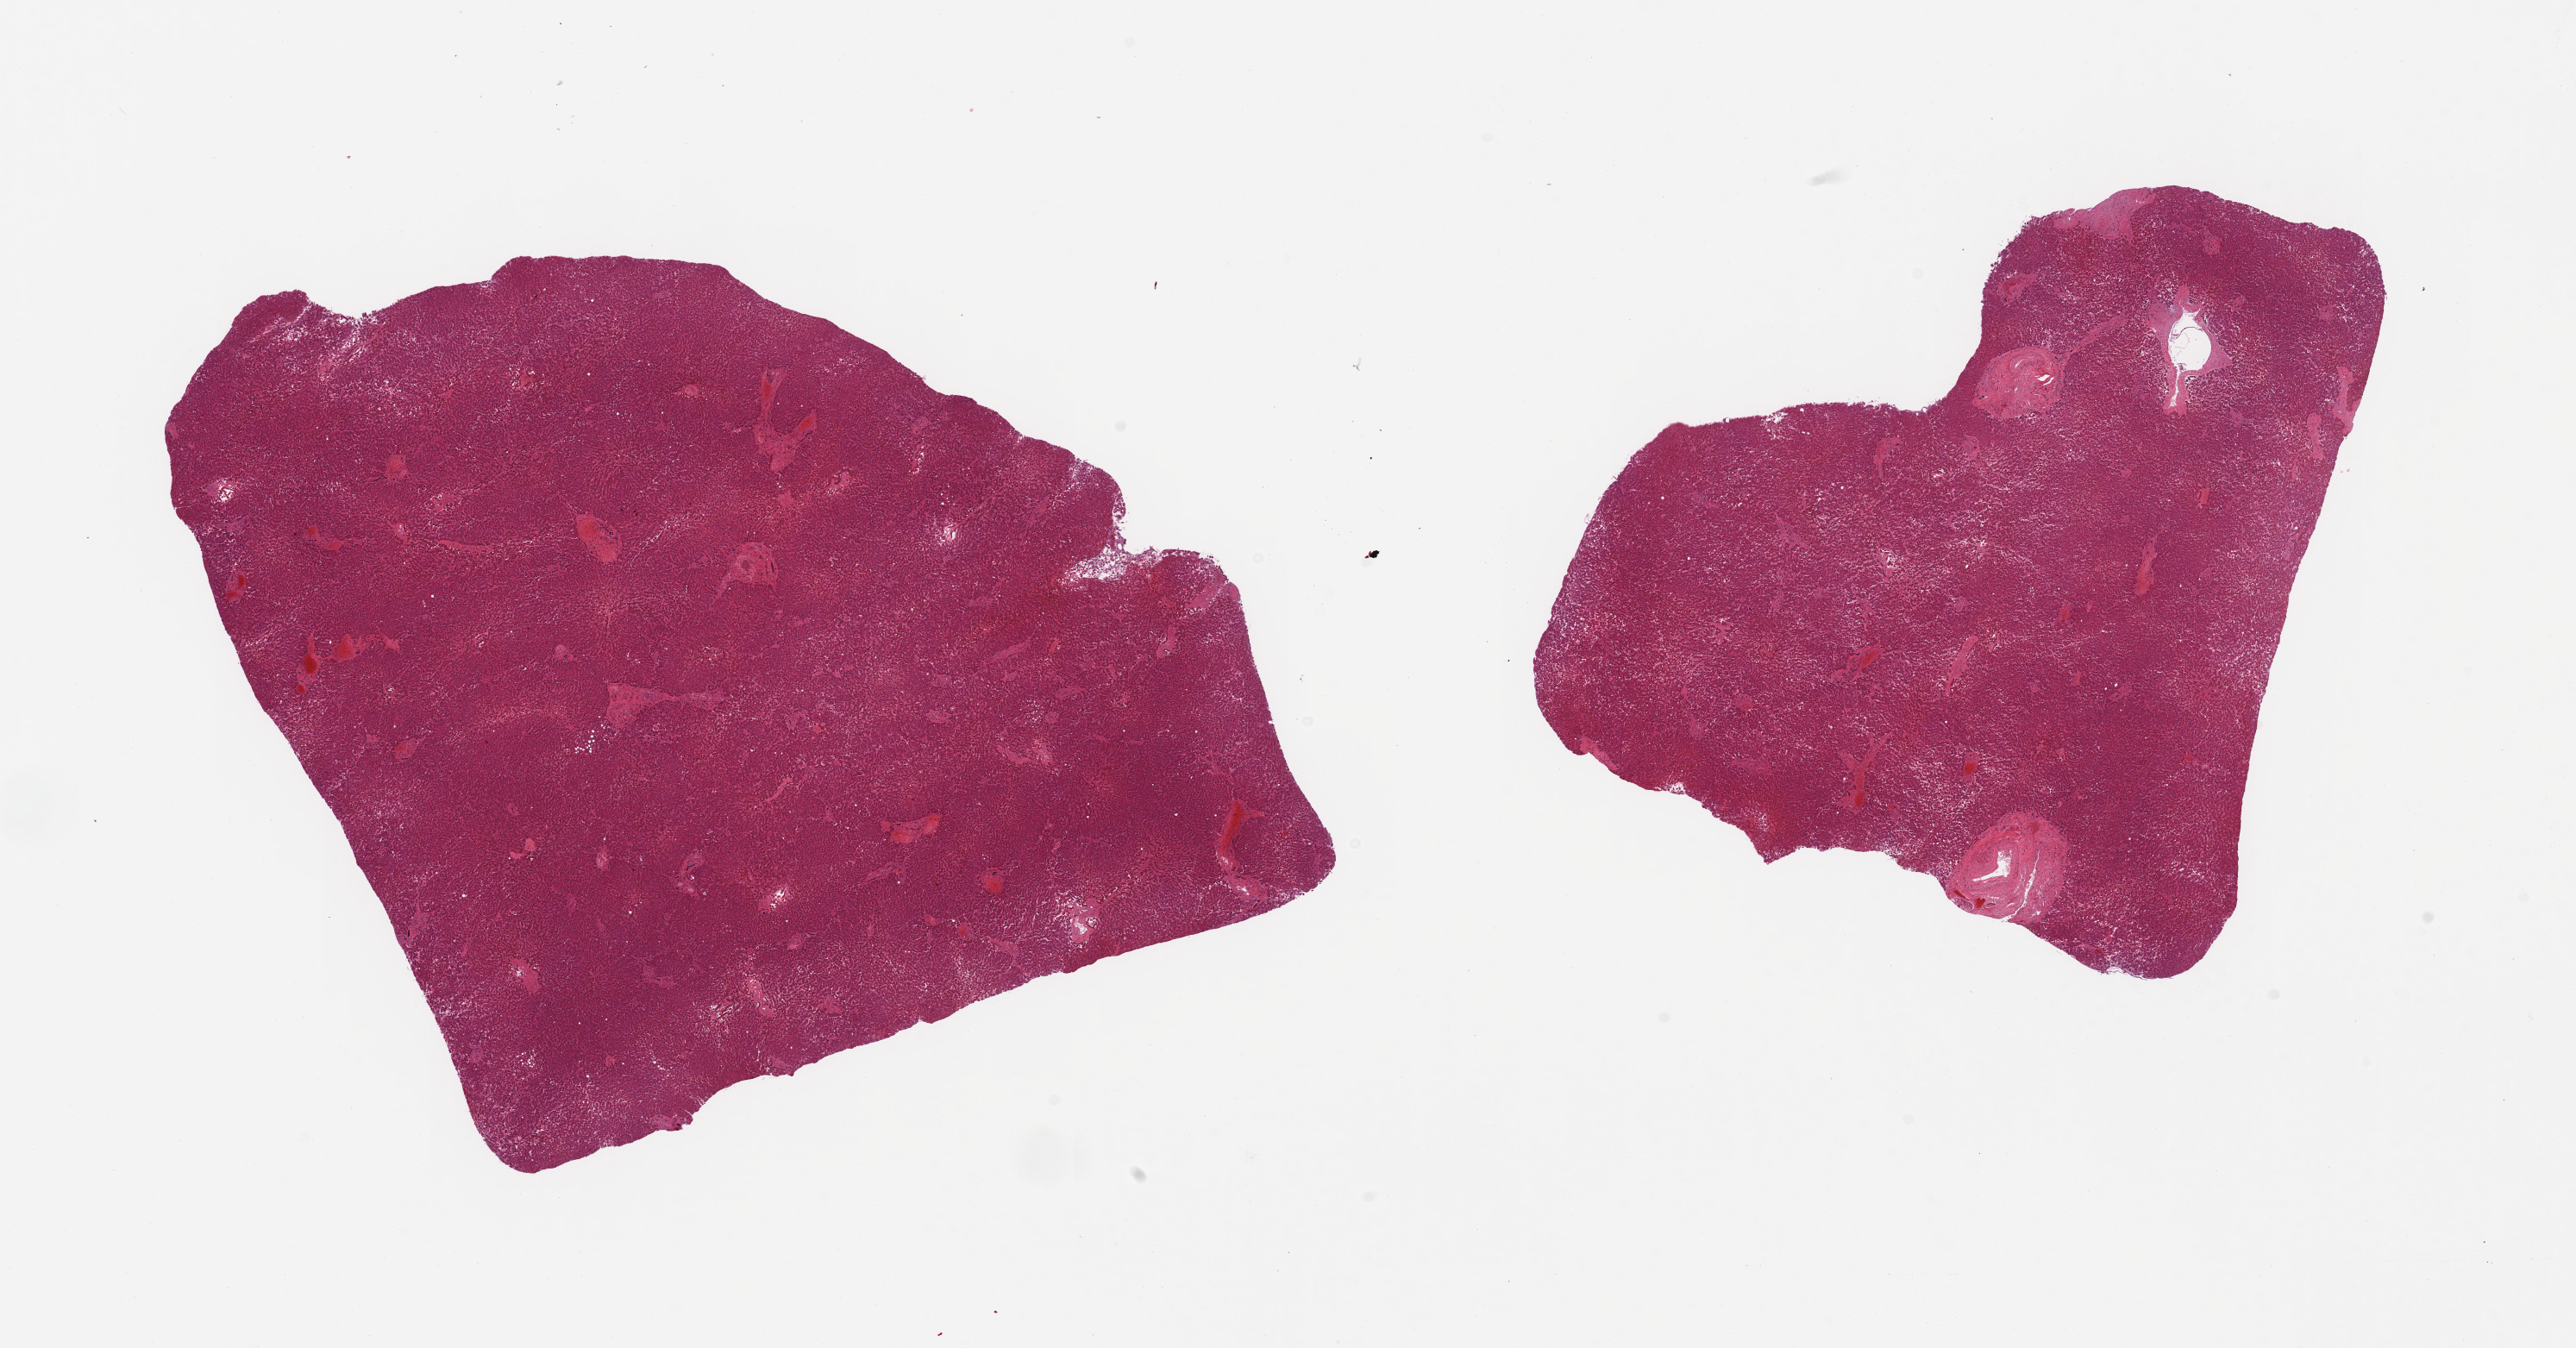
Digitized hematoxylin and eosin (H&E)-stained section — a low-resolution overview of the entire scanned area, about 23.6 x 12.4 mm, PAXgene-fixed, paraffin-embedded tissue, sampled site (target tissue): liver, donor tissue sample. Donor: female.
Review note (as recorded): 2 pieces; focally moderate autolysis.